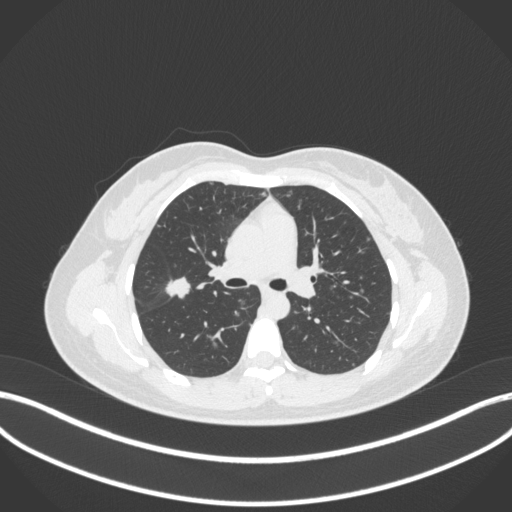
Chest CT, one axial slice. Position 206 of 214 along the scan axis. Lung window (W 1500 / L -600 HU). 1 mm slice thickness. 512 × 512 image matrix. Patient: female, 33 years. From the clinical record (not read from this slice): clinical TNM (as recorded): T1c N0 M0; histopathological grade: G2-G3.
Annotated regions visible in this slice (rectangle marked by the reading radiologist):
- lung tumour (recorded histology: adenocarcinoma): box from (x=163, y=271) to (x=193, y=302) px